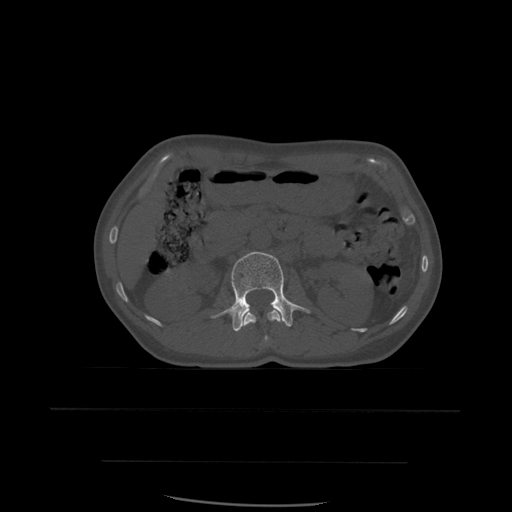
CT including the spine, one axial slice. Slice 232 of 574 in the series (ordered by position). Bone window (W 1800 / L 400 HU). 1.25 mm slice thickness. 512 × 512 image matrix. Patient age 48 years. Case-level facts recorded for this patient, not image findings: primary cancer: lung.
Structures marked on this image (semi-automatic segmentation, software-assisted and operator-edited):
- L1 vertebra: bounding box <242,309,282,343> (left, top, right, bottom; pixels)
- L2 vertebra: <211,252,311,332>